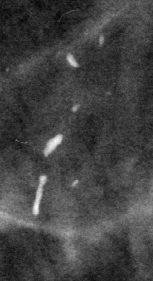
Region of interest cut from a scanned film mammogram (one marked finding), right breast, MLO view, BI-RADS breast density category 1 (scale 1–4).
- Calcifications, distribution regional; BI-RADS assessment category 2; subtlety rating 3 on a 1 (subtle) to 5 (obvious) scale; benign; no additional work-up was recommended (benign without callback).